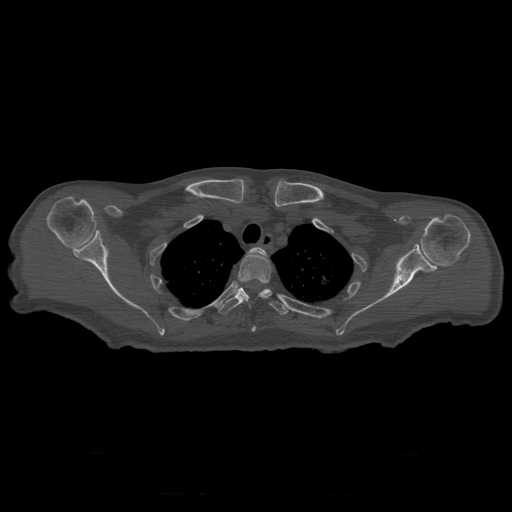
CT including the spine, one axial slice. Position 253 of 397 along the scan axis. 120 kVp. Bone window (W 1800 / L 400 HU). 512 × 512 image matrix, field of view 510 × 510 mm. Patient age 73 years. Case-level facts recorded for this patient, not image findings: primary cancer: prostate.
Annotated regions visible in this slice (semi-automatically segmented with operator editing):
- T2 vertebra: box from (x=250, y=247) to (x=267, y=258) px
- T3 vertebra: (x=238, y=252)–(x=272, y=332)
- T4 vertebra: (x=219, y=288)–(x=288, y=315)